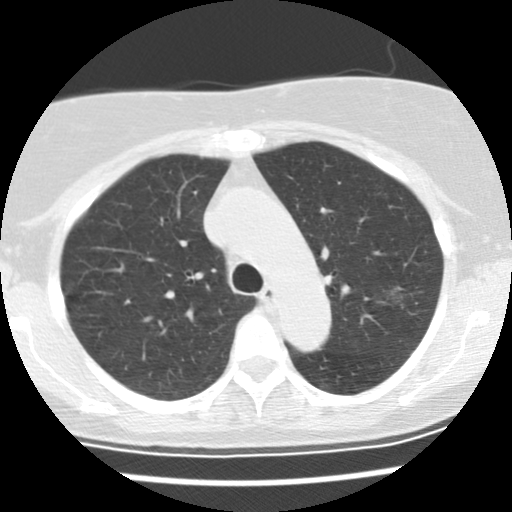
Low-dose screening chest CT, axial slice. Baseline annual screen. Lung window (W 1500 / L -600 HU). 2.5 mm slice thickness. Slice 101 of 137 in the series. 512 × 512 image matrix. Female, age 66 years at enrolment. Former smoker at enrolment.
Expert-annotated lung lesion, bounding box <373,277,429,326> (left, top, right, bottom; pixels). The exam's reader record, not a measurement of the box and not confirmed to be the same lesion: non-calcified nodule or mass ≥4 mm, left upper lobe, 25 × 17 mm, poorly defined margins, mixed attenuation. Official screen result: positive, change unspecified: nodule(s) >= 4 mm or enlarging nodule(s), mass(es), or other non-specific abnormalities suspicious for lung cancer. Later outcome: lung cancer diagnosed 44 days after this screen — bronchiolo-alveolar adenocarcinoma, NOS, left upper lobe, well differentiated (G1), stage IA (AJCC 6th edition), 19 mm at pathology.